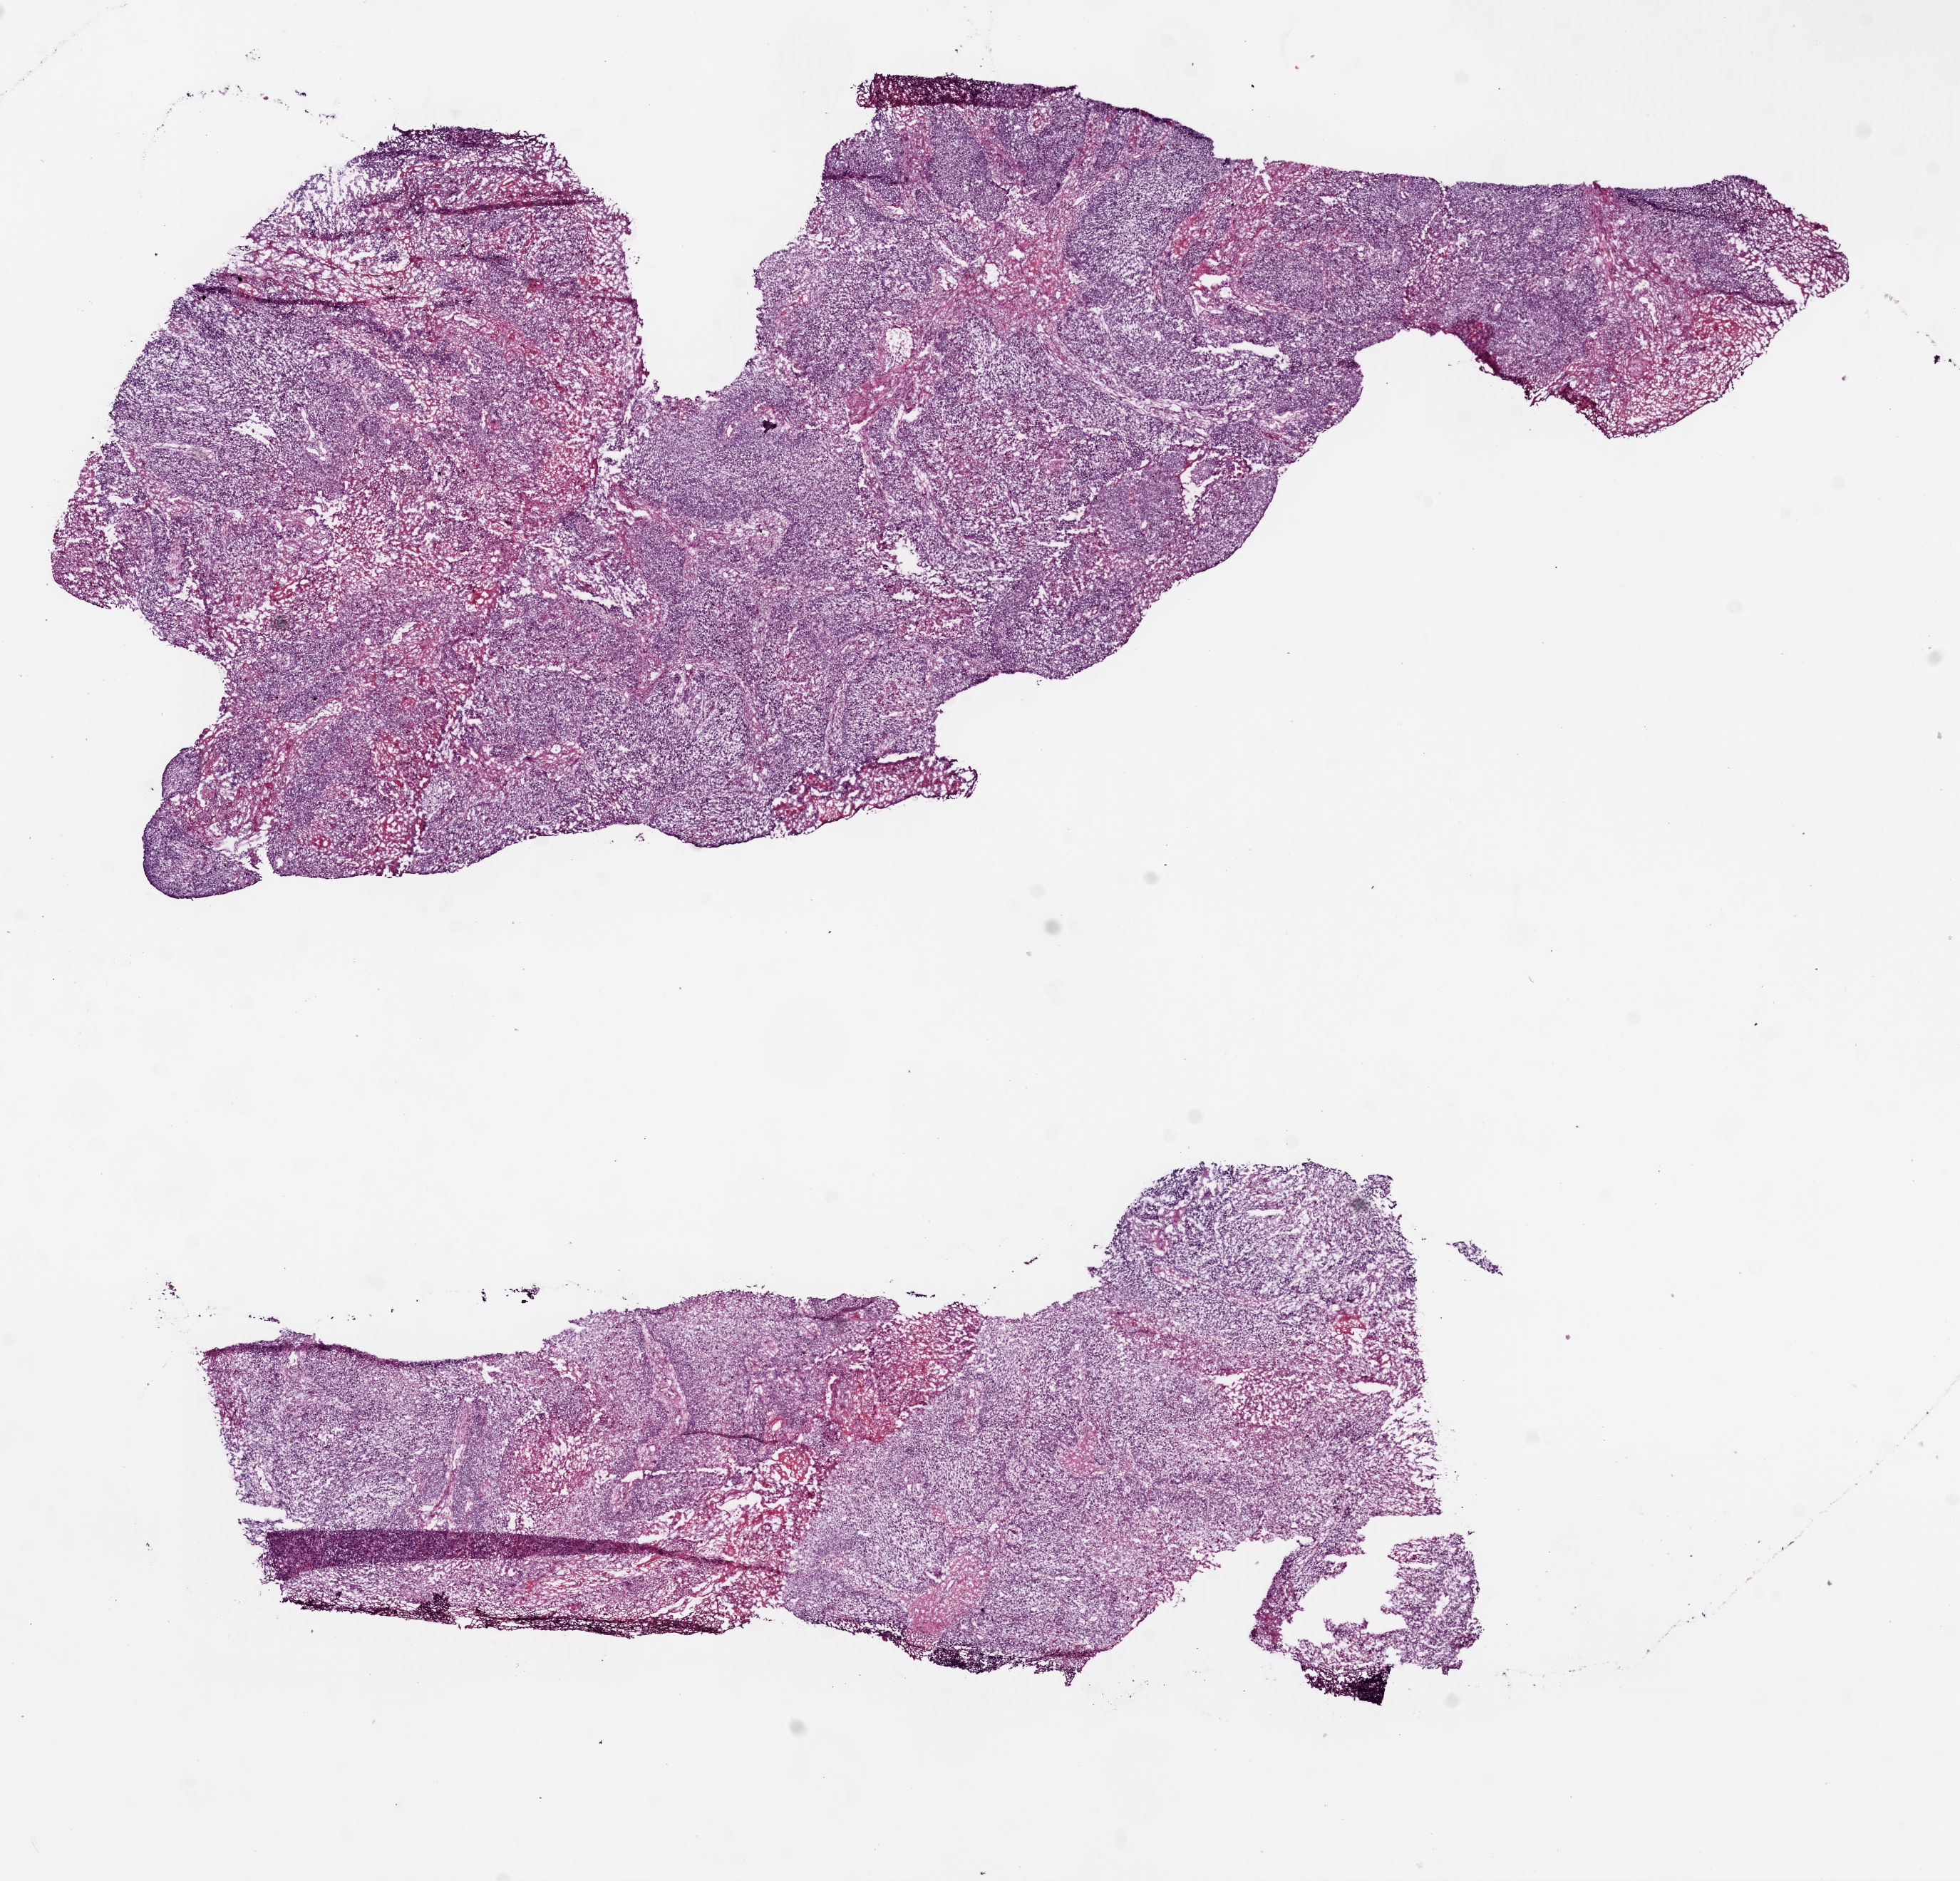
Hematoxylin and eosin (H&E) stained whole-slide image — low-resolution overview of the scanned area, about 11.0 x 10.6 mm (from a 20x scan); frozen section from the bottom of the tissue portion; sample: primary tumour, head and neck. Male, age 56 years at initial diagnosis. Histologic grade: G2 (moderately differentiated). Slide review estimates, as recorded: tumour cells 80%, tumour nuclei 80%, normal cells 0%, stromal cells 20%, necrosis 0%.
TNM: T4a N0. AJCC pathologic stage: IVA. Diagnosis: Squamous cell carcinoma, NOS (larynx, NOS).